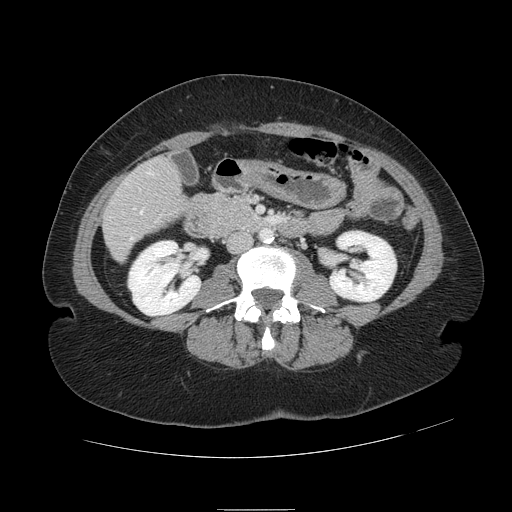
Contrast-enhanced abdominal CT, one axial slice; slice 22 of 121 in the series (ordered by position); soft-tissue window (W 400 / L 40 HU); 512 × 512 image matrix, field of view 400 × 400 mm. Female patient, age 52 years. Case-level facts recorded for this patient, not image findings: diagnosis: colorectal cancer liver metastases, imaged before liver resection; multiple liver metastases: yes; largest metastasis: 6.3 cm.
Outlined on this slice (manually delineated by an expert):
- hepatic veins: bounding box <130,172,153,240> (left, top, right, bottom; pixels)
- liver: <105,159,179,260>
- portal vein (with intrahepatic branches): <134,208,136,210>